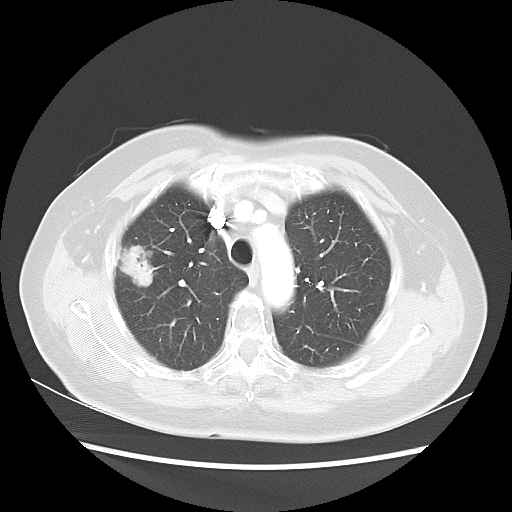
Chest CT, one axial slice. Slice 36 of 48 in the series (ordered by position). Reconstruction kernel LUNG. Lung window (W 1500 / L -600 HU). 5 mm slice thickness. 512 × 512 image matrix, field of view 360 × 360 mm. Patient: female, 75 years. From the clinical record (not read from this slice): clinical TNM (as recorded): T1c N0 M0.
Outlined on this slice (rectangle marked by the reading radiologist):
- lung tumour (recorded histology: adenocarcinoma): bounding box (x1, y1, x2, y2) in pixels: (117, 241, 158, 298)